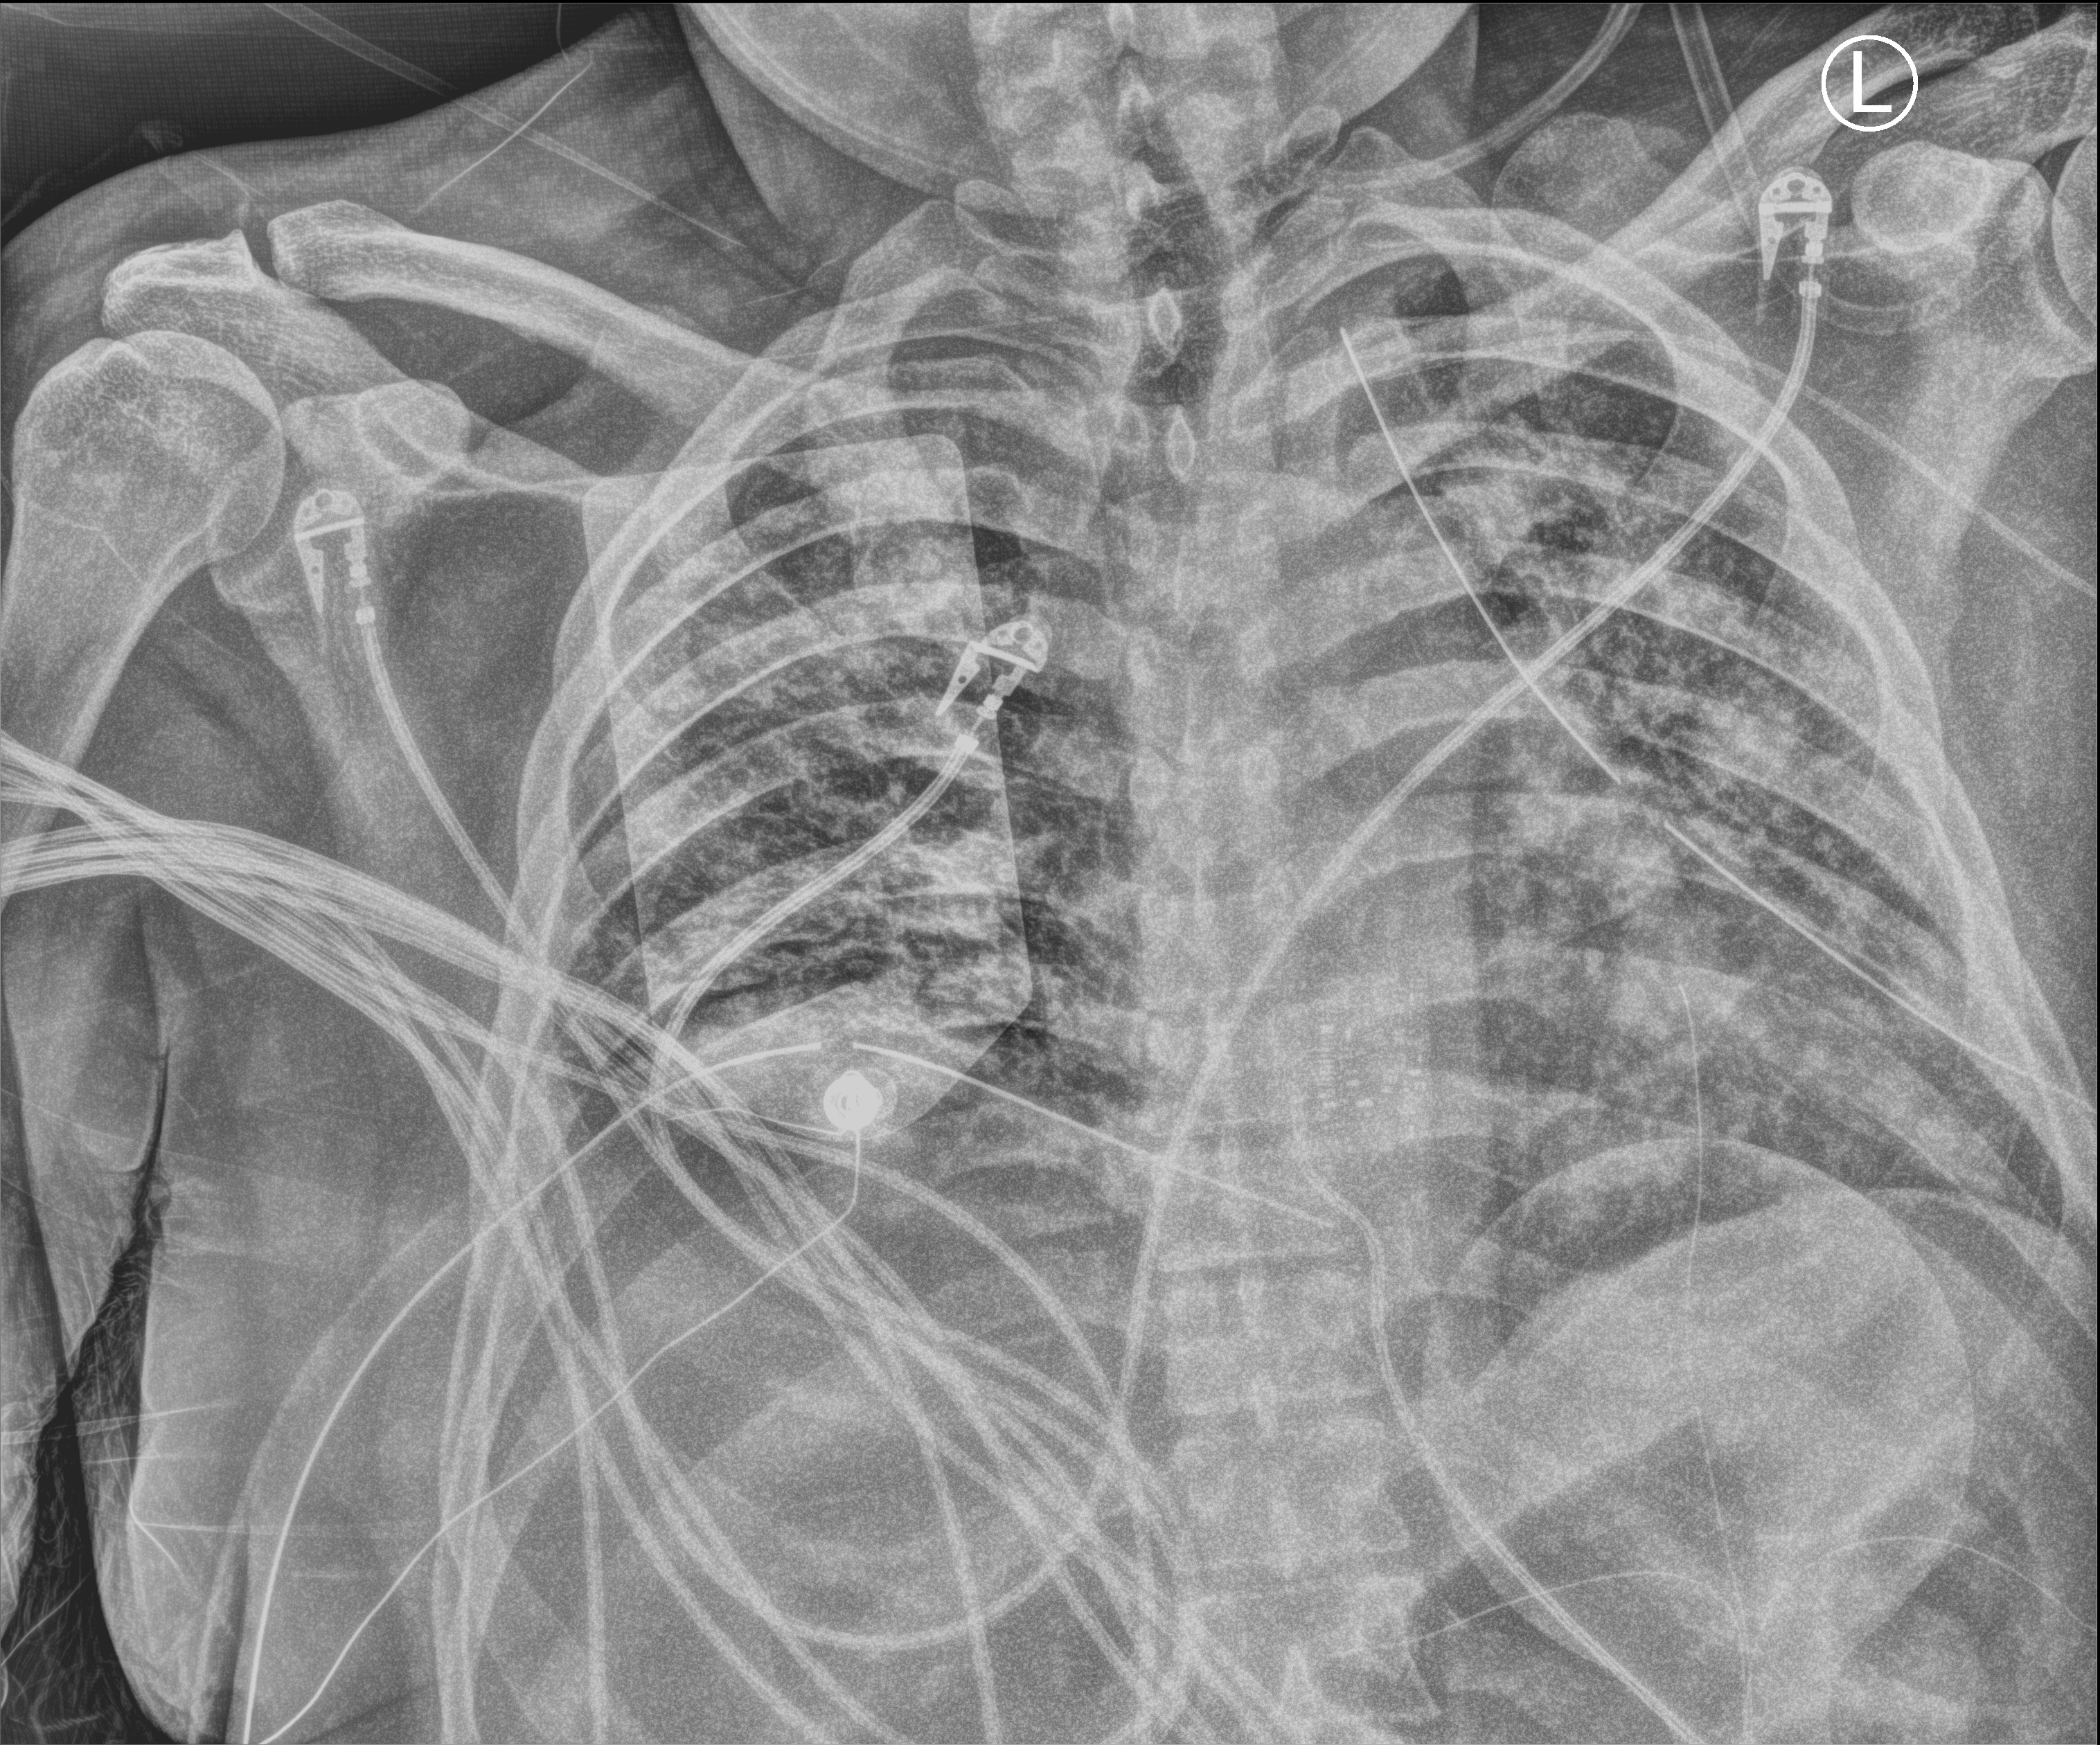
Bedside chest radiograph (computed radiography), anteroposterior (AP) projection. Patient hospitalised with COVID-19; male, aged 18–59 years.
Hospital-stay facts (about this admission, not read from this image; timing relative to this image not recorded): mechanically ventilated during this hospital stay: yes; admitted to intensive care during this hospital stay: yes.